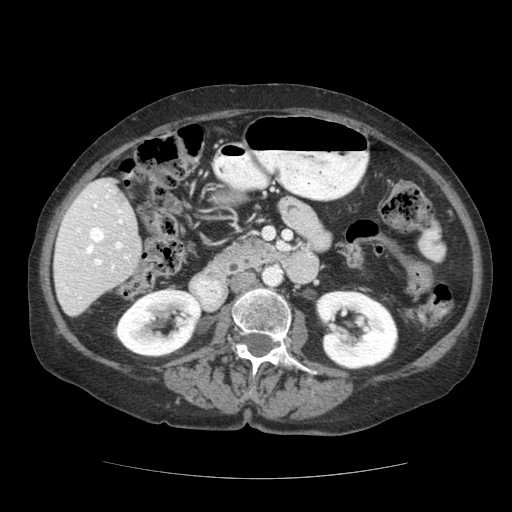
Contrast-enhanced abdominal CT (liver protocol), one axial slice; slice 54 of 111 in the series (ordered by position); soft-tissue window (W 400 / L 40 HU); 2.5 mm slice thickness; 512 × 512 image matrix. Case-level facts recorded for this patient, not image findings: diagnosis: hepatocellular carcinoma (patient treated with transarterial chemoembolisation; whether this scan precedes or follows treatment is not stated here); TNM stage (as recorded): Stage-I.
Structures marked on this image (semi-automatic segmentation, software-assisted and operator-edited):
- liver parenchyma outside the tumour (the mass and vessels are separate outlines, so this box may not span the whole liver): bounding box [x1, y1, x2, y2] px = [54, 178, 140, 316]
- liver vessels: [57, 184, 129, 291]